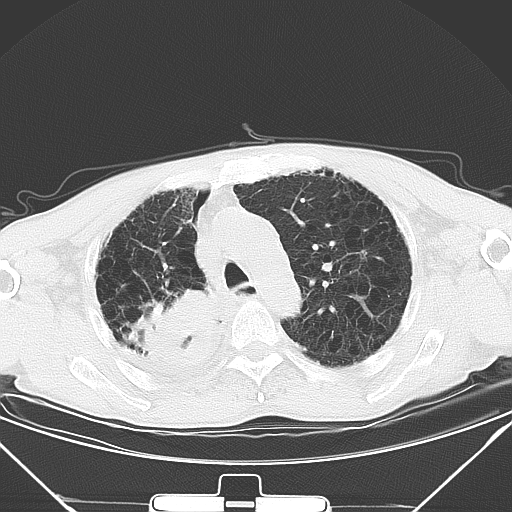
Chest CT, one axial slice; position 36 of 50 along the scan axis; 120 kVp; lung window (W 1500 / L -600 HU); 5 mm slice thickness; 512 × 512 image matrix, field of view 373 × 373 mm. Male patient, age 65 years. Case-level facts recorded for this patient, not image findings: clinical TNM (as recorded): T3 N1 M1a.
Outlined on this slice (rectangle marked by the reading radiologist):
- lung tumour (recorded histology: squamous cell carcinoma): bounding box (x1, y1, x2, y2) in pixels: (139, 286, 221, 374)